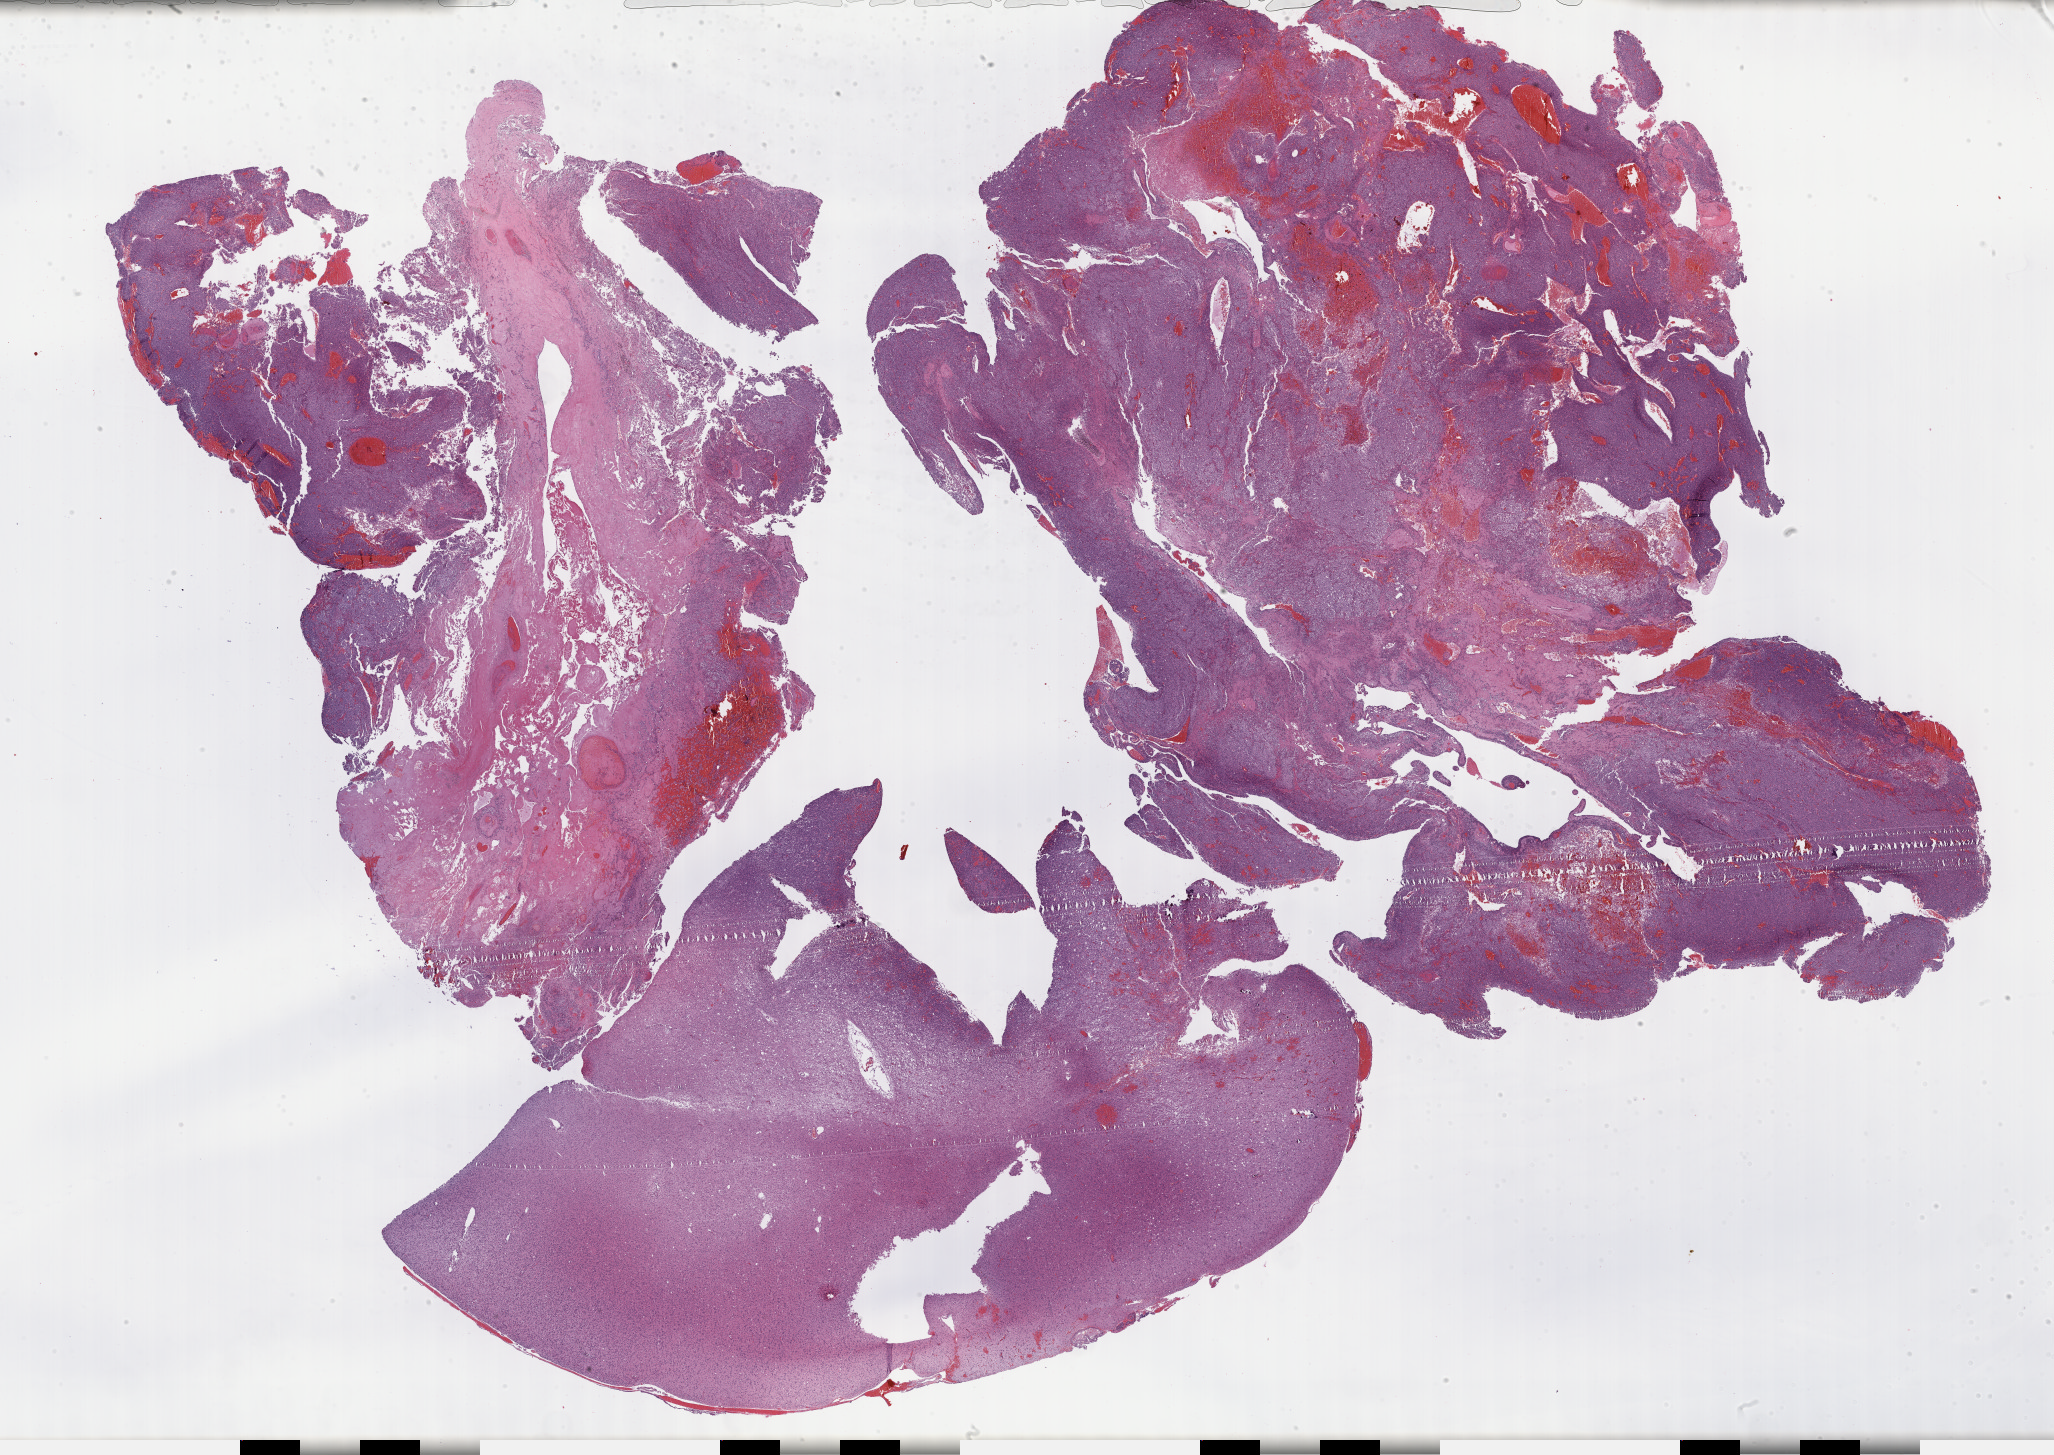
Whole-slide histology image, H&E-stained — low-resolution overview of the scanned area, about 33.2 x 23.5 mm. Formalin-fixed paraffin-embedded (FFPE) diagnostic section. Primary tumour sample from the brain. Patient: male, age at initial diagnosis 33 years. Histologic grade: G3 (poorly differentiated).
• laterality: left
• histologic diagnosis: Oligodendroglioma, anaplastic (cerebrum)